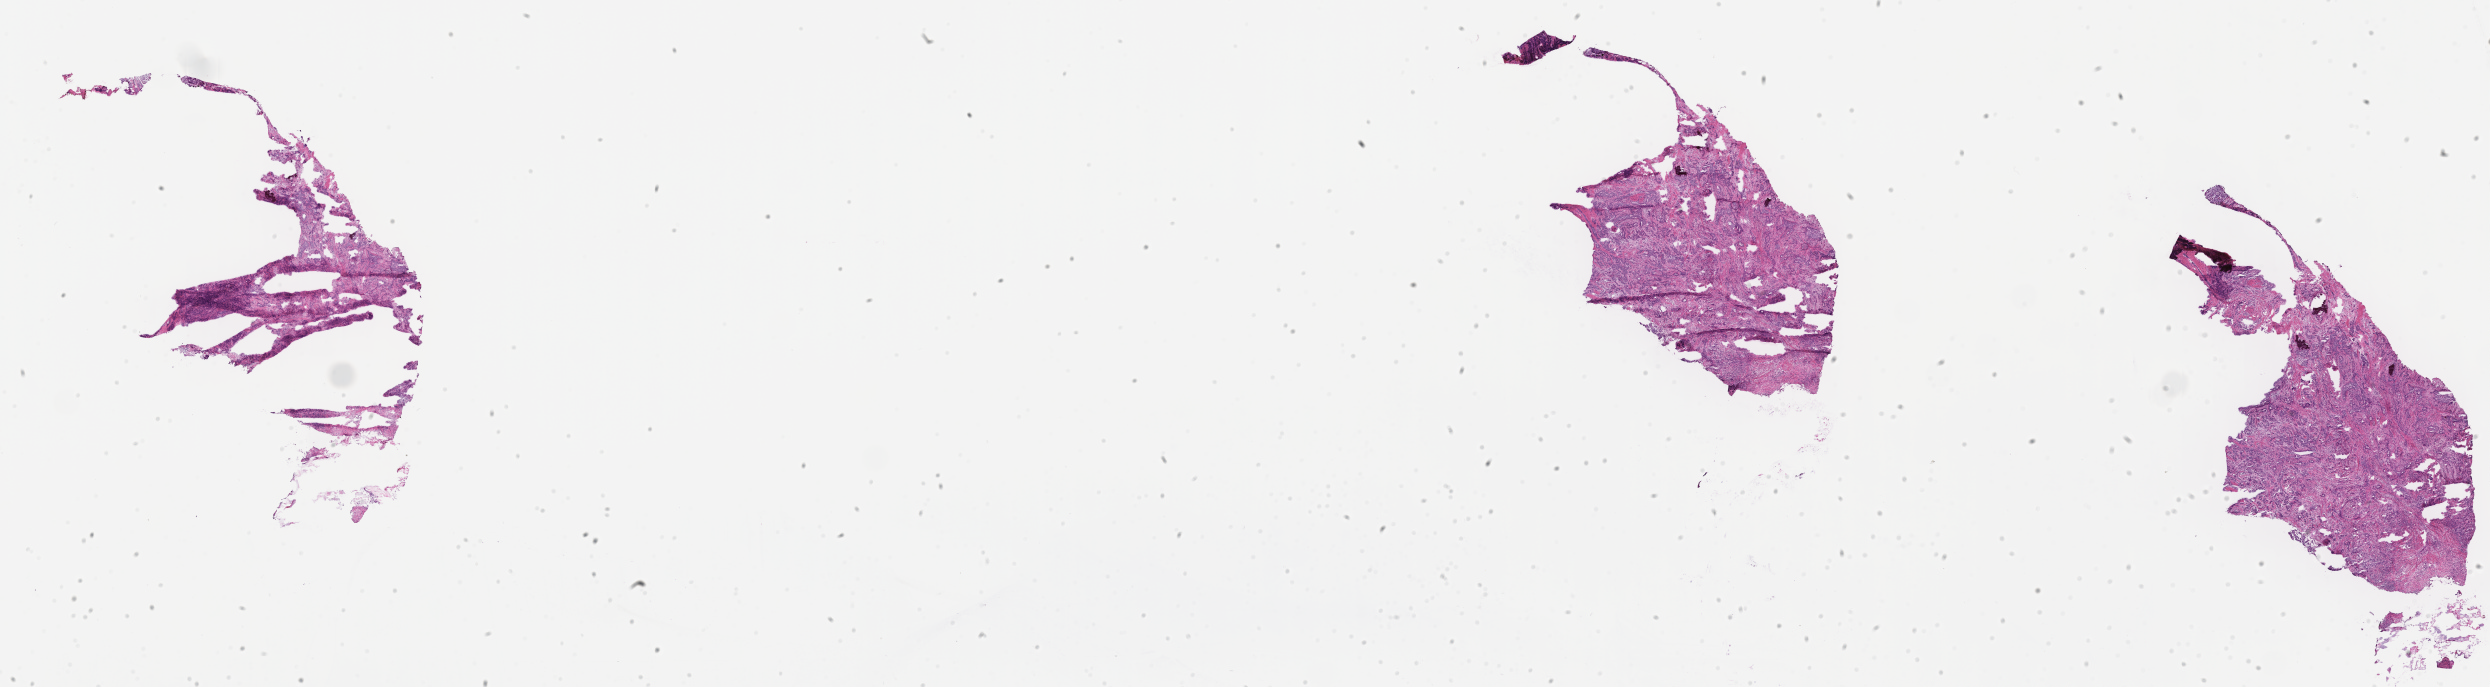
H&E whole-slide image — whole scanned area (about 40.2 x 11.1 mm) shown as a low-resolution overview. Frozen section (tissue freezing medium). Primary tumor. Site: breast (right). Female patient; age at initial diagnosis 52 years. Slide review estimates, as recorded: tumor cells 50%, tumor nuclei 50%.
Diagnosis: Infiltrating duct carcinoma, NOS.